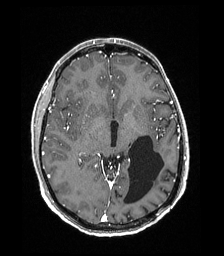
Brain MRI from a brain-tumour surgery series, one axial slice; slice 100 of 192 in the series (ordered by position); T1-weighted post-contrast; 1 mm slice thickness; 224 × 256 image matrix. From the clinical record (not read from this slice): histopathology: Low grade glioma; IDH mutation: no; tumour location: Left Parieto-Occipital Intraventricular.
Annotated regions visible in this slice (outlined manually by an expert reader):
- previous resection cavity: box from (x=124, y=135) to (x=164, y=204) px